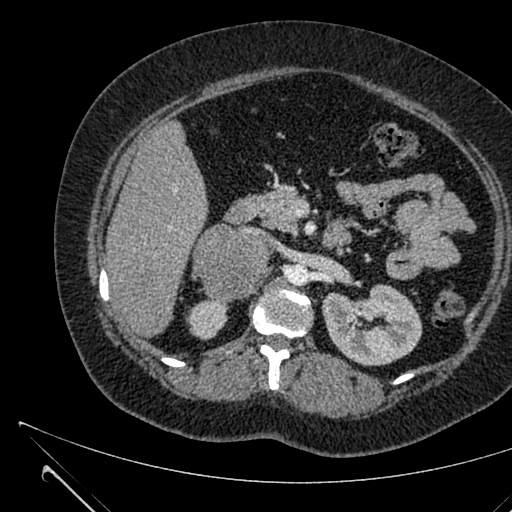
Contrast-enhanced abdominal CT, one axial slice; position 381 of 731 along the scan axis; intravenous contrast given; soft-tissue window (W 400 / L 40 HU); 1 mm slice thickness; 512 × 512 image matrix, field of view 376 × 376 mm. Patient: female, 36 years. Case-level facts recorded for this patient, not image findings: diagnosis: adrenocortical carcinoma; tumour side: right adrenal; tumour size at pathology: 10 cm.
Outlined on this slice (semi-automatically segmented with operator editing):
- mass: bounding box [x1, y1, x2, y2] px = [194, 224, 268, 300]